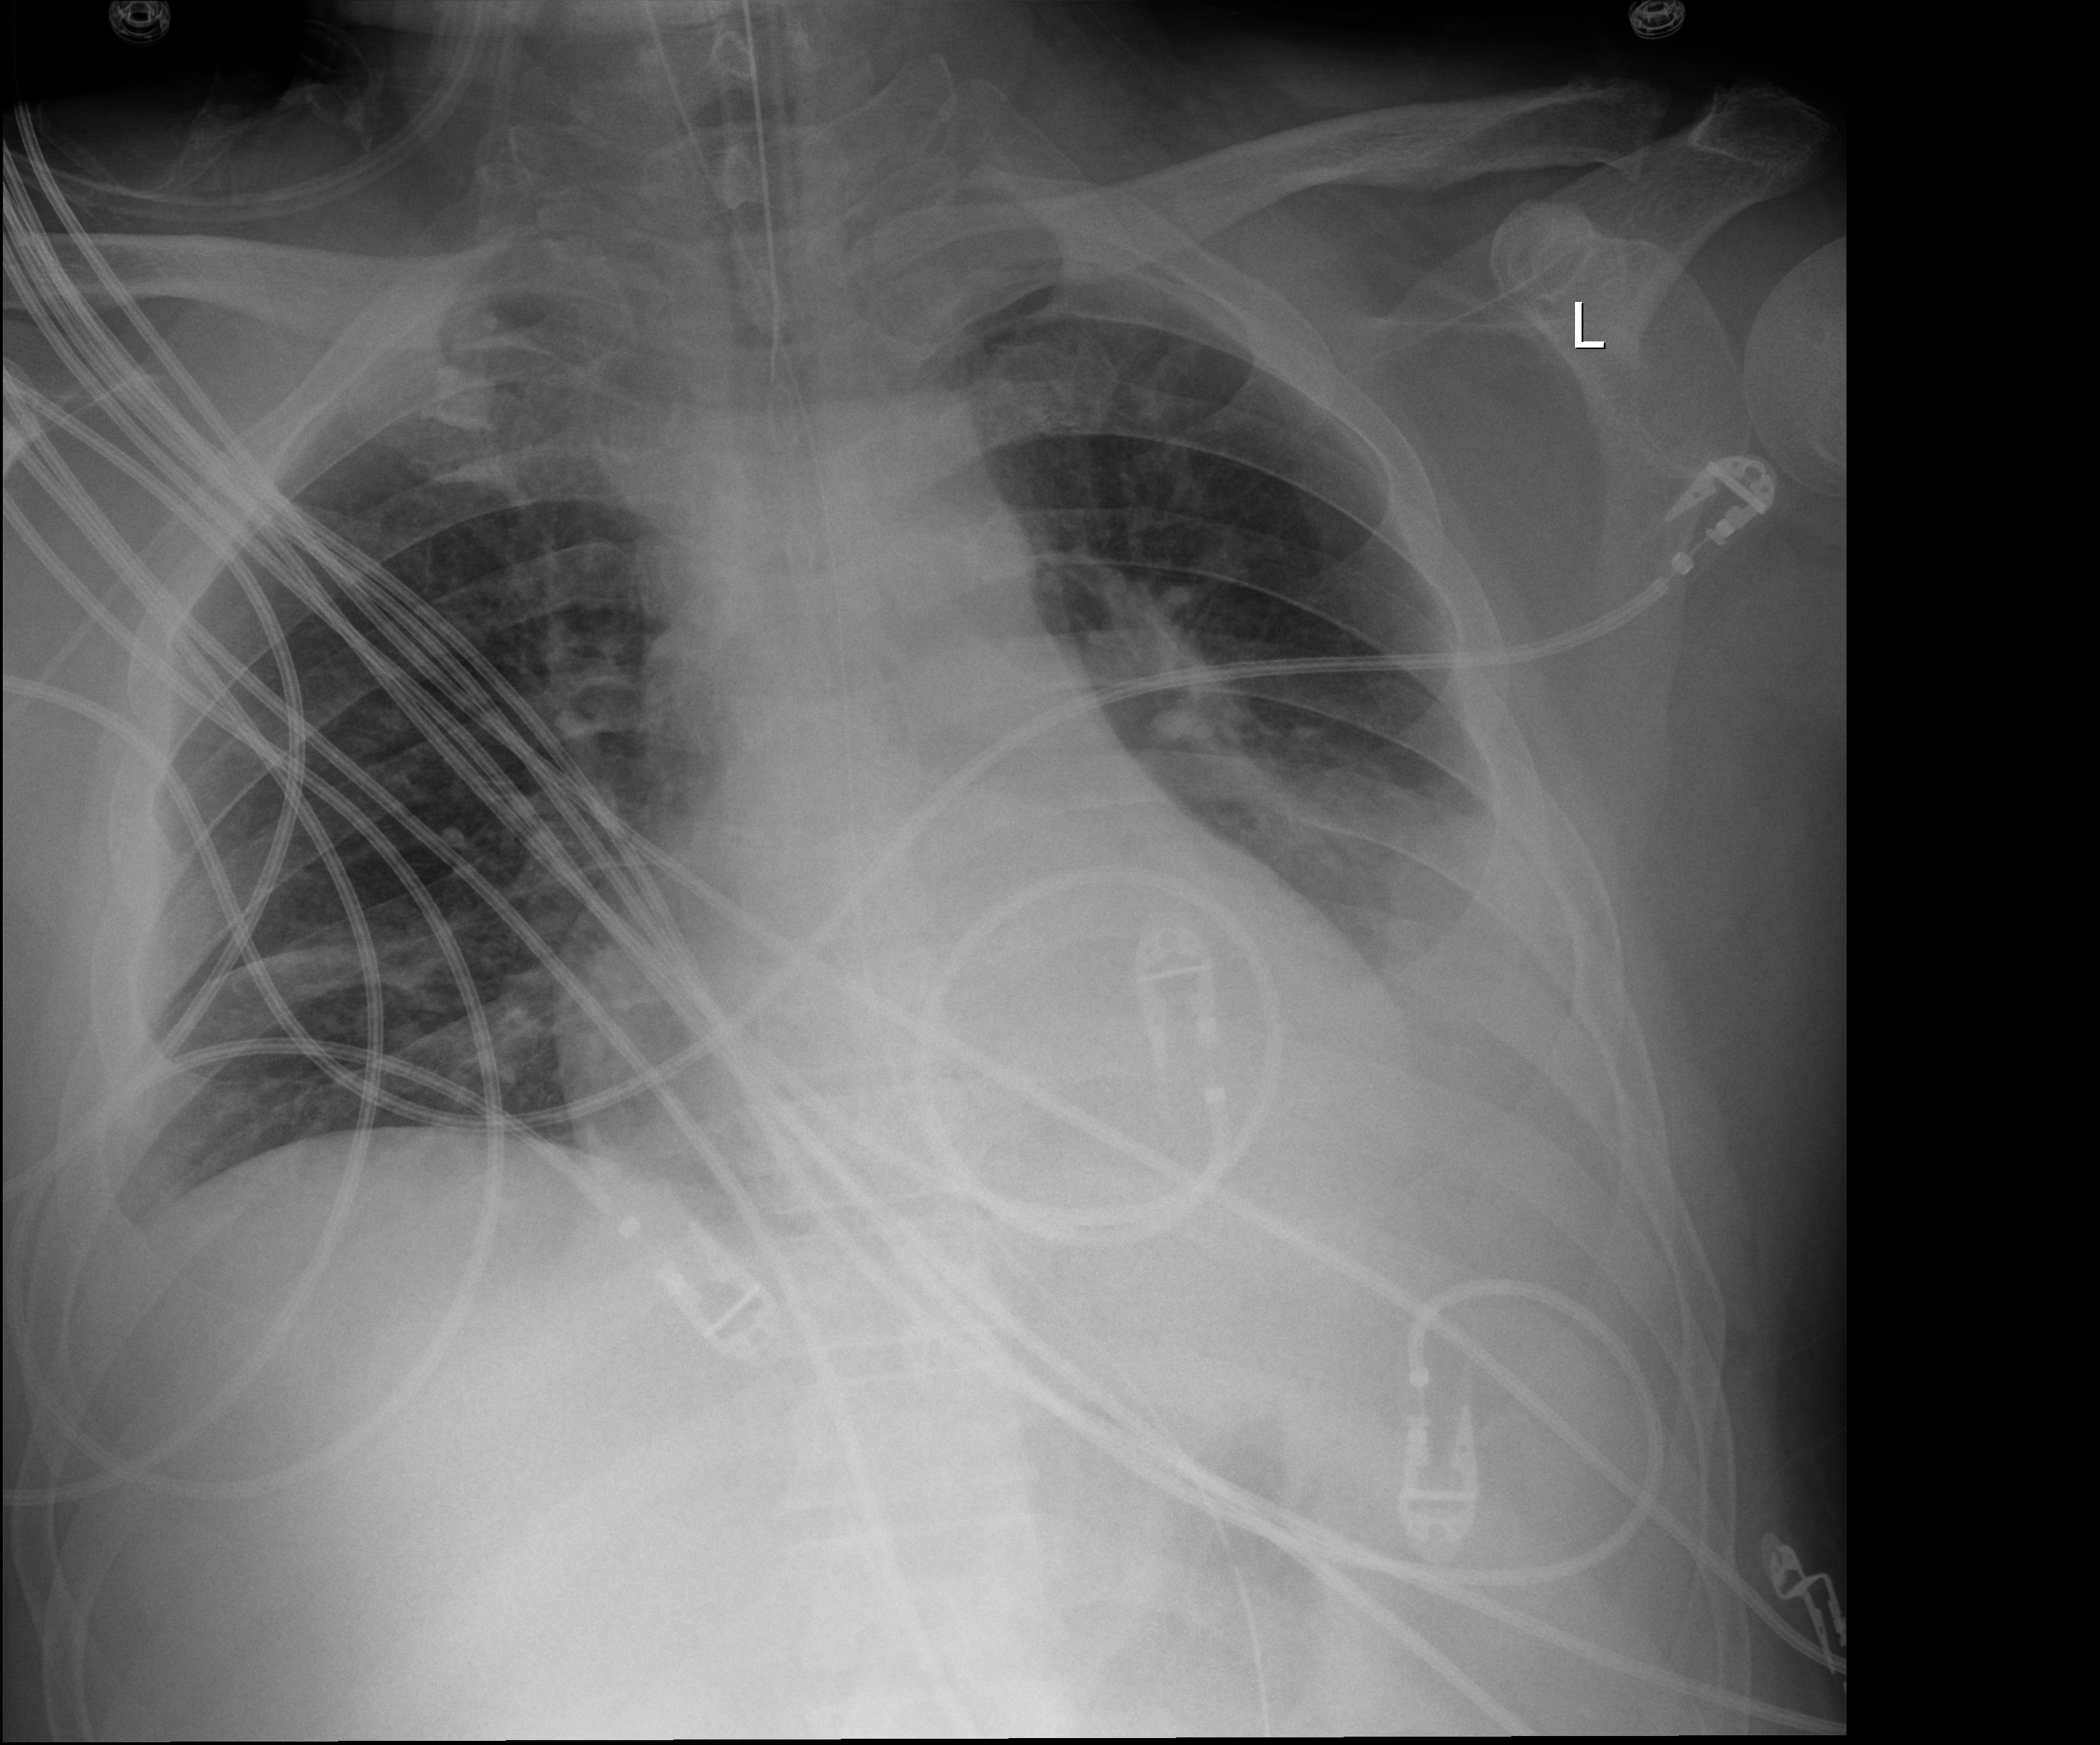
Chest radiograph, anteroposterior (AP) projection. Patient hospitalised with COVID-19; male, aged 18–59 years.
From the hospital-stay record, not from the radiograph (when in the stay this image was taken is not recorded): admitted to intensive care during this hospital stay: yes; mechanically ventilated during this hospital stay: yes.